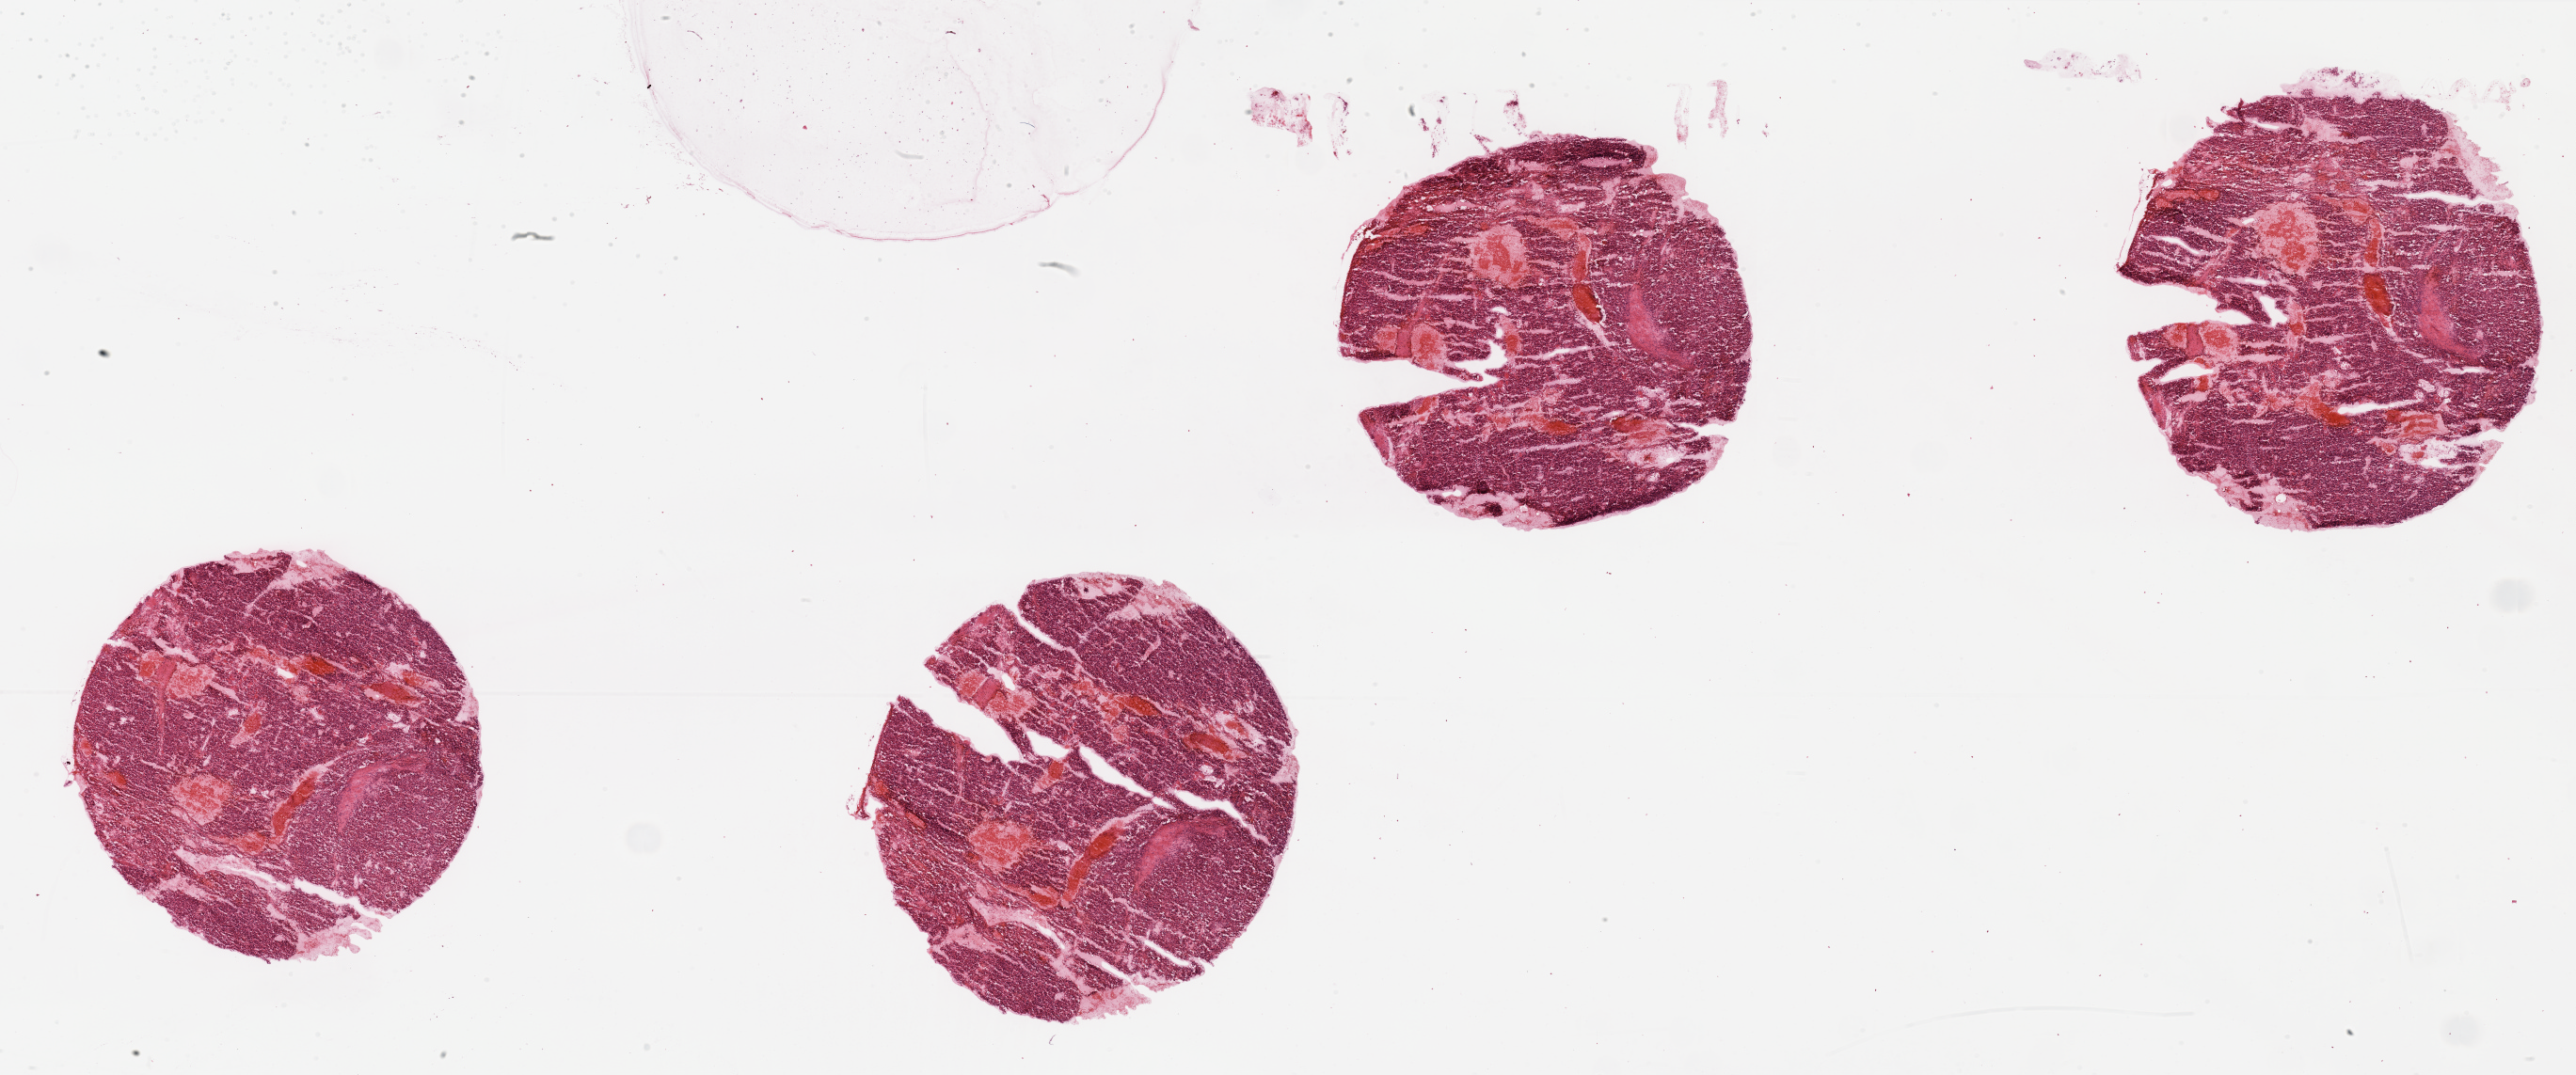
Digitized H&E tissue section (whole slide), whole scanned area (about 43.3 x 18.1 mm, from a 20x scan) shown as a low-resolution overview. Tumour tissue sample, sampled site: kidney. Male, 66 y/o. Histologic grade: G2 (moderately differentiated). Pathologist review of this section (percent, as recorded): tumour nuclei 90%, necrosis 5%.
• primary tumour site (as recorded): upper pole
• diagnosis: Renal cell carcinoma, NOS
• AJCC pathologic stage: I